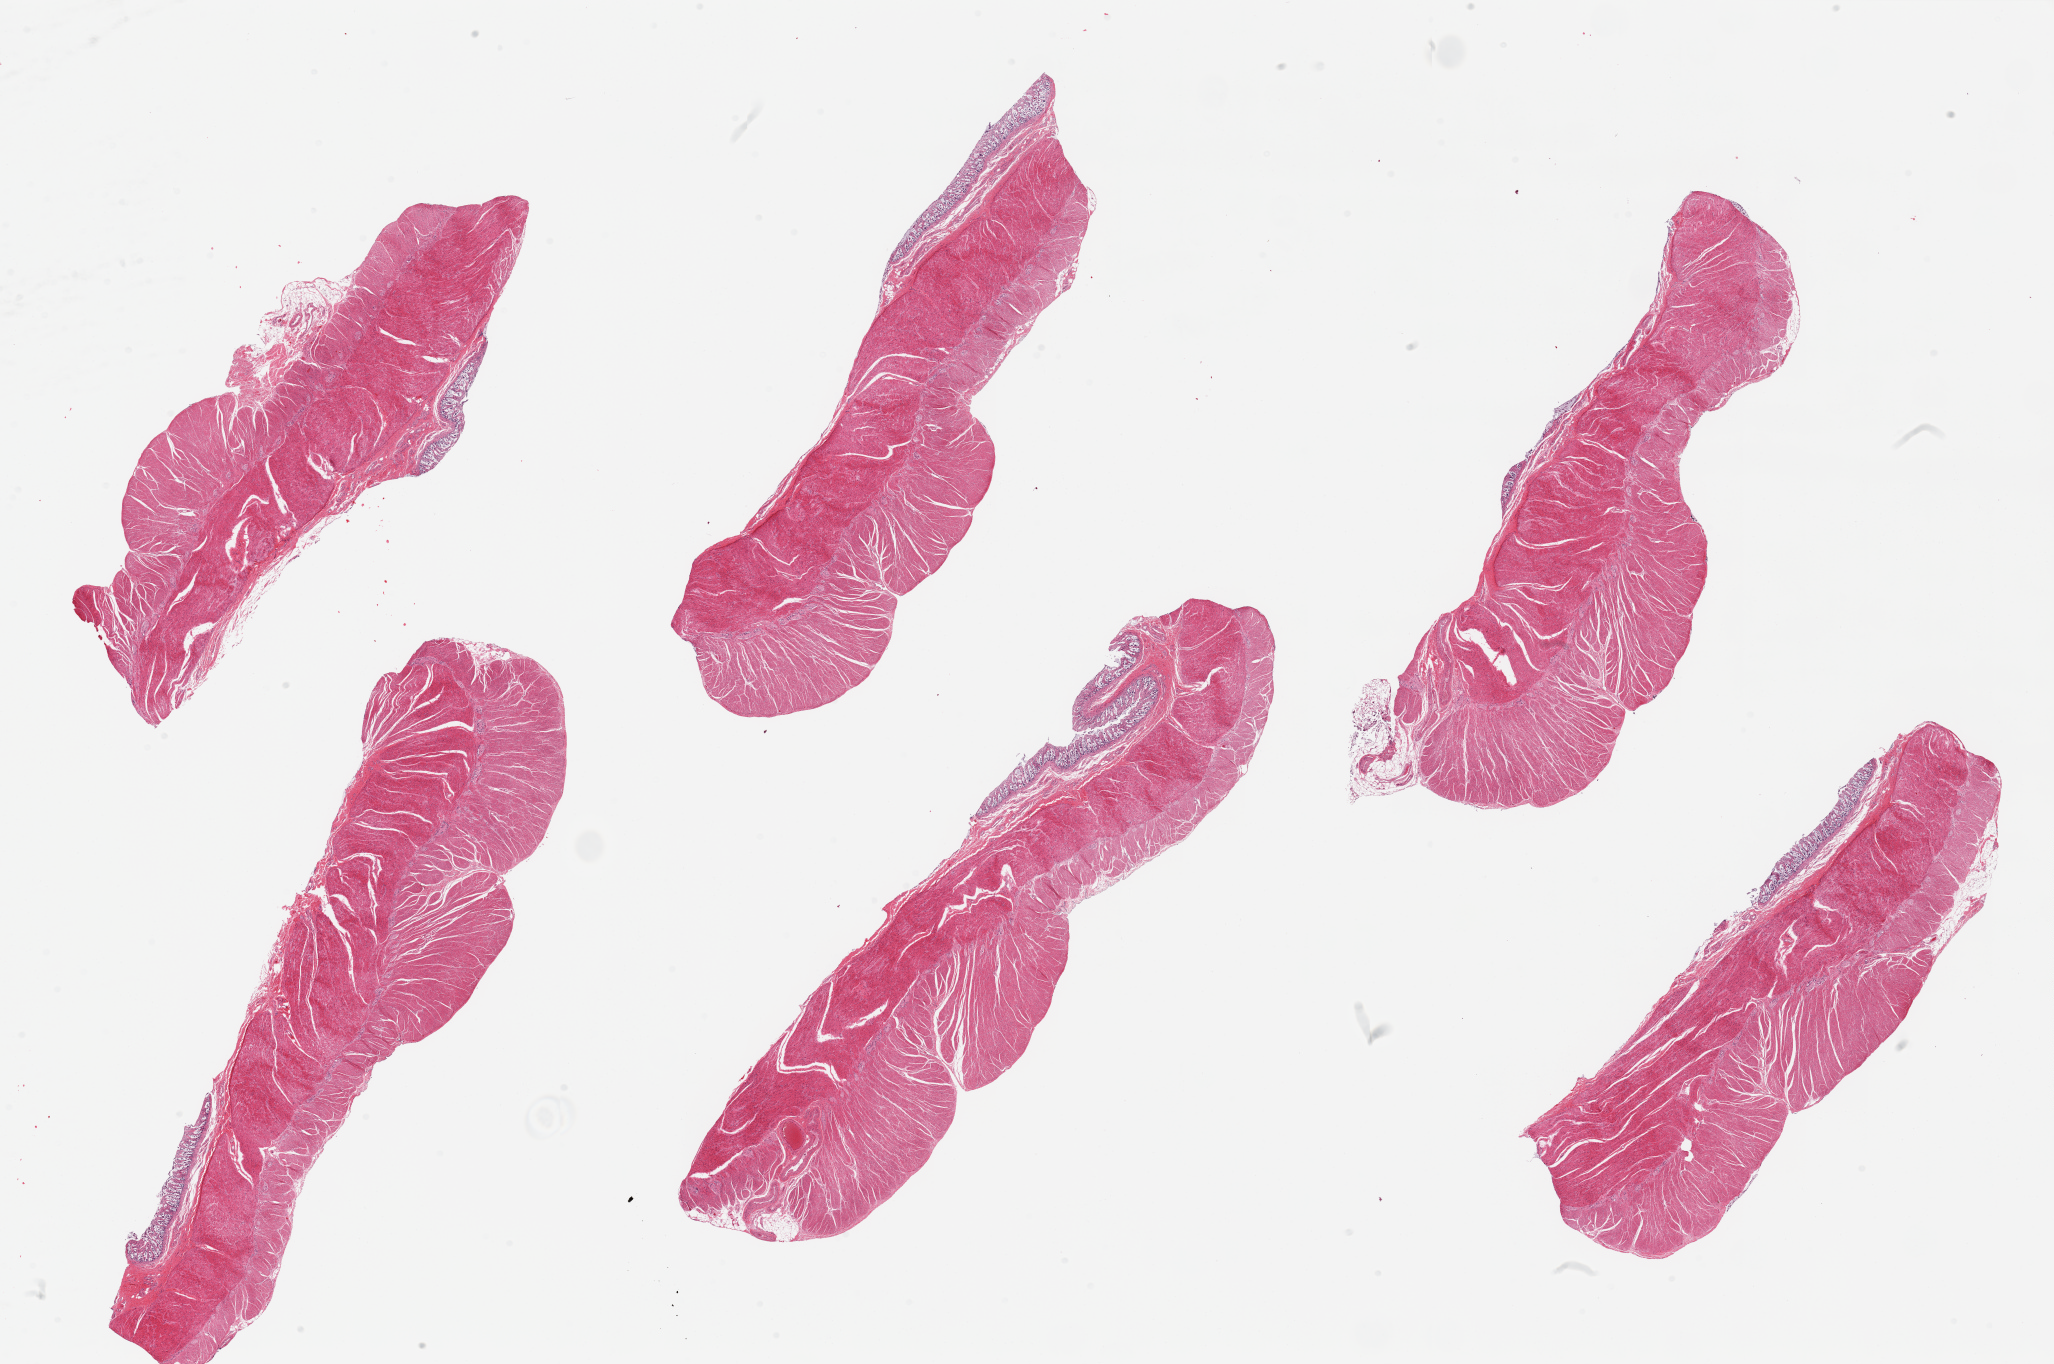
Digitized hematoxylin and eosin (H&E)-stained section — low-resolution overview of the scanned area, about 32.5 x 21.6 mm (from a 20x scan); PAXgene-fixed, paraffin-embedded tissue; sampled site (target tissue): sigmoid colon; donor tissue sample. Donor: male.
Pathologist's review note for this sample: 6 pieces, muscularis, few foci of autolyzed mucosa.